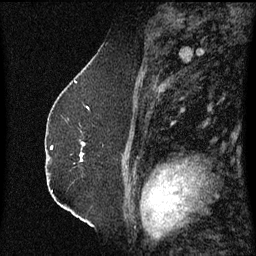
Breast MRI (dynamic contrast-enhanced), one sagittal slice. Position 39 of 60 along the scan axis. Dynamic contrast-enhanced series, image 2 of 3 at this slice position (ordered by acquisition). 1.5 T. TE 4.2 ms, TR 8.4 ms. 2.3 mm slice thickness. 256 × 256 image matrix. Patient: female, 52 years. Case-level facts recorded for this patient, not image findings: setting: breast cancer imaged before/during neoadjuvant chemotherapy; receptor status: HR-positive, HER2-negative.
Structures marked on this image (semi-automatic segmentation, software-assisted and operator-edited):
- analysis volume of interest (the breast-tissue region the enhancement analysis was run in; not a lesion): bounding box [x1, y1, x2, y2] px = [68, 118, 86, 163]
- tumour enhancement mask (voxels above the 70 % enhancement threshold inside the analysis volume of interest): [81, 142, 85, 161]